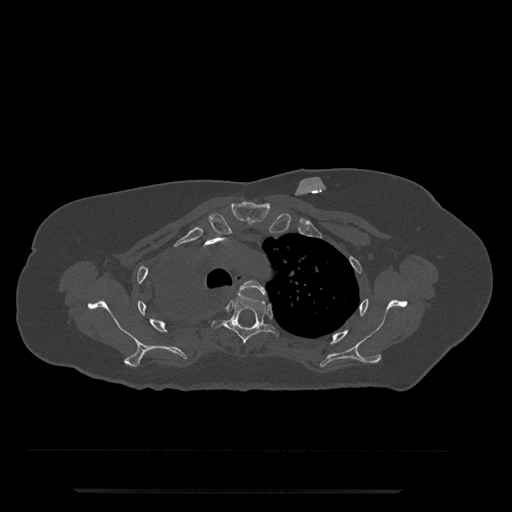
CT including the spine, one axial slice. Slice 595 of 797 in the series (ordered by position). Reconstruction kernel Br40s/3. Bone window (W 1800 / L 400 HU). 0.5 mm slice thickness. 512 × 512 image matrix, field of view 440 × 440 mm. Female patient, age 51 years. From the clinical record (not read from this slice): primary cancer: neuro; vertebrae with lytic lesions (as recorded): T8.
Outlined on this slice (semi-automatic segmentation, software-assisted and operator-edited):
- T3 vertebra: bounding box <239,280,266,297> (left, top, right, bottom; pixels)
- T4 vertebra: <211,293,279,344>